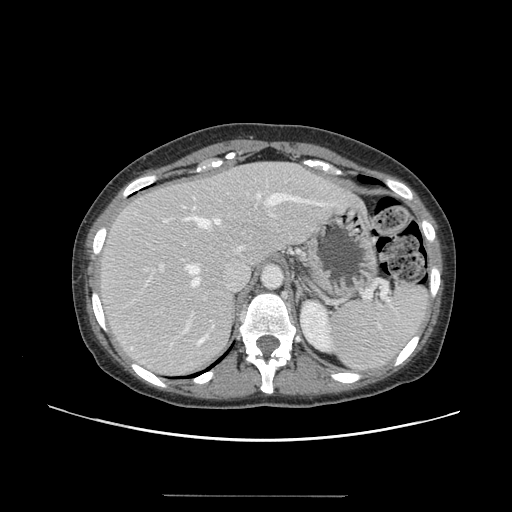
Contrast-enhanced abdominal CT, one axial slice. Position 106 of 144 along the scan axis. 120 kVp. Intravenous contrast given. Soft-tissue window (W 400 / L 40 HU). 2.5 mm slice thickness. 512 × 512 image matrix, field of view 380 × 380 mm. Female patient, age 53 years. From the clinical record (not read from this slice): diagnosis: colorectal cancer liver metastases, imaged before liver resection; multiple liver metastases: yes; largest metastasis: 1.1 cm; disease in both lobes: no.
Annotated regions visible in this slice (manually delineated by an expert):
- hepatic veins: box from (x=185, y=193) to (x=321, y=286) px
- liver: (x=99, y=162)–(x=359, y=375)
- planned liver remnant (the part of the liver to remain after resection): (x=96, y=162)–(x=299, y=301)
- portal vein (with intrahepatic branches): (x=160, y=211)–(x=275, y=317)